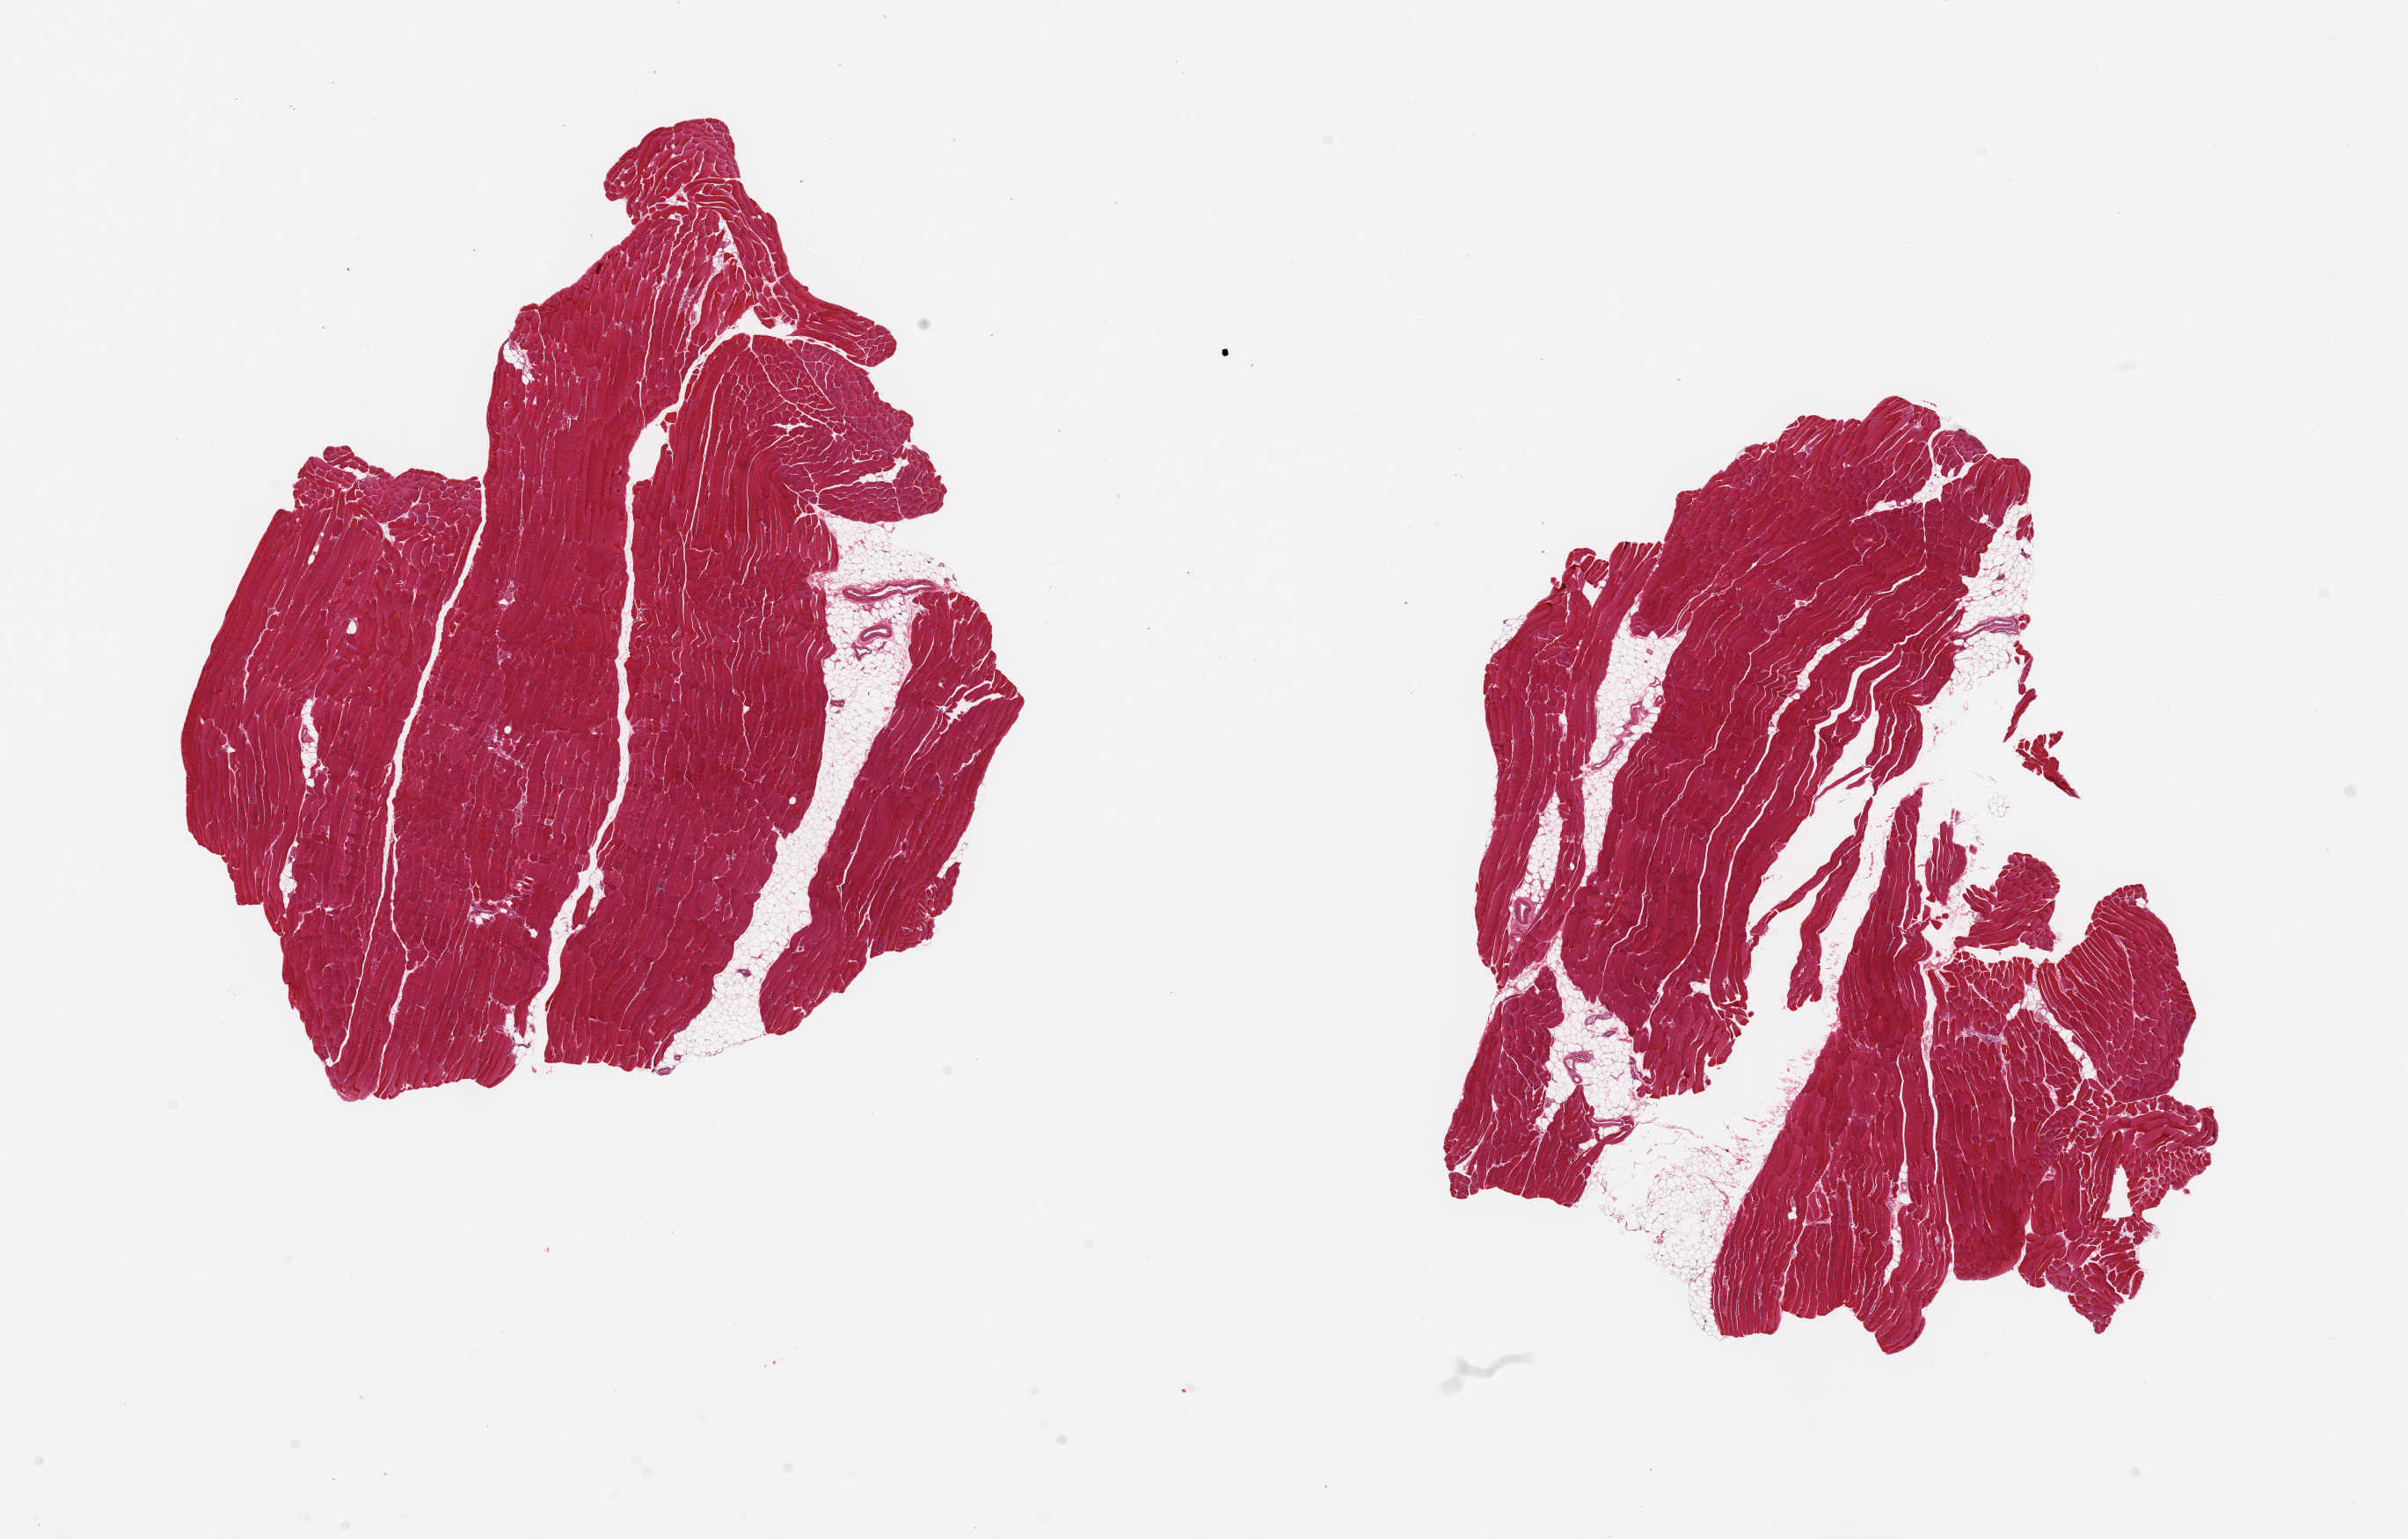
Whole-slide image, haematoxylin and eosin stain, shown as a low-resolution overview of the whole scanned area (about 21.7 x 13.8 mm), PAXgene-fixed, paraffin-embedded tissue, target tissue: skeletal muscle, donor tissue sample. Female donor.
Pathologist's review note for this sample: 2 pieces; 5% internal fat.